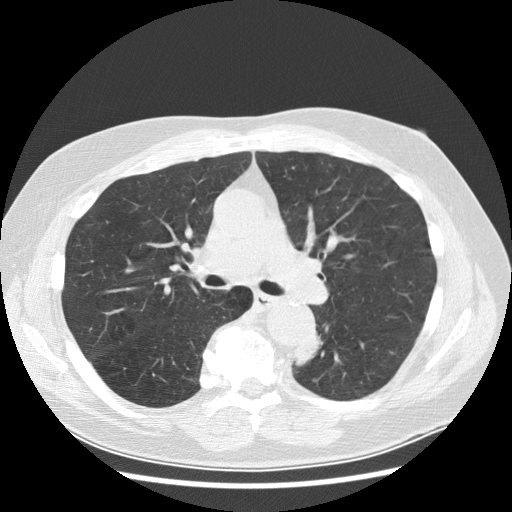
Low-dose screening chest CT, axial slice. Baseline screening round. Lung window (W 1500 / L -600 HU). 2.5 mm slice thickness. 120 kVp. Slice 109 of 282 in the series. Male, age 70 years at enrolment. Current smoker at enrolment.
Expert-annotated lung lesion, box from (x=279, y=326) to (x=331, y=384) px. The exam's reader record, not a measurement of the box and not confirmed to be the same lesion: non-calcified nodule or mass ≥4 mm, left lower lobe, 27 × 16 mm, spiculated (stellate) margins, soft tissue attenuation, pre-existing on the prior screen: yes; interval growth: yes. Official screen result: positive, change unspecified: nodule(s) >= 4 mm or enlarging nodule(s), mass(es), or other non-specific abnormalities suspicious for lung cancer. Later outcome: lung cancer diagnosed 97 days after this screen — papillary adenocarcinoma, NOS, left lower lobe, moderately differentiated (G2), stage IB (AJCC 6th edition), 35 mm at pathology.